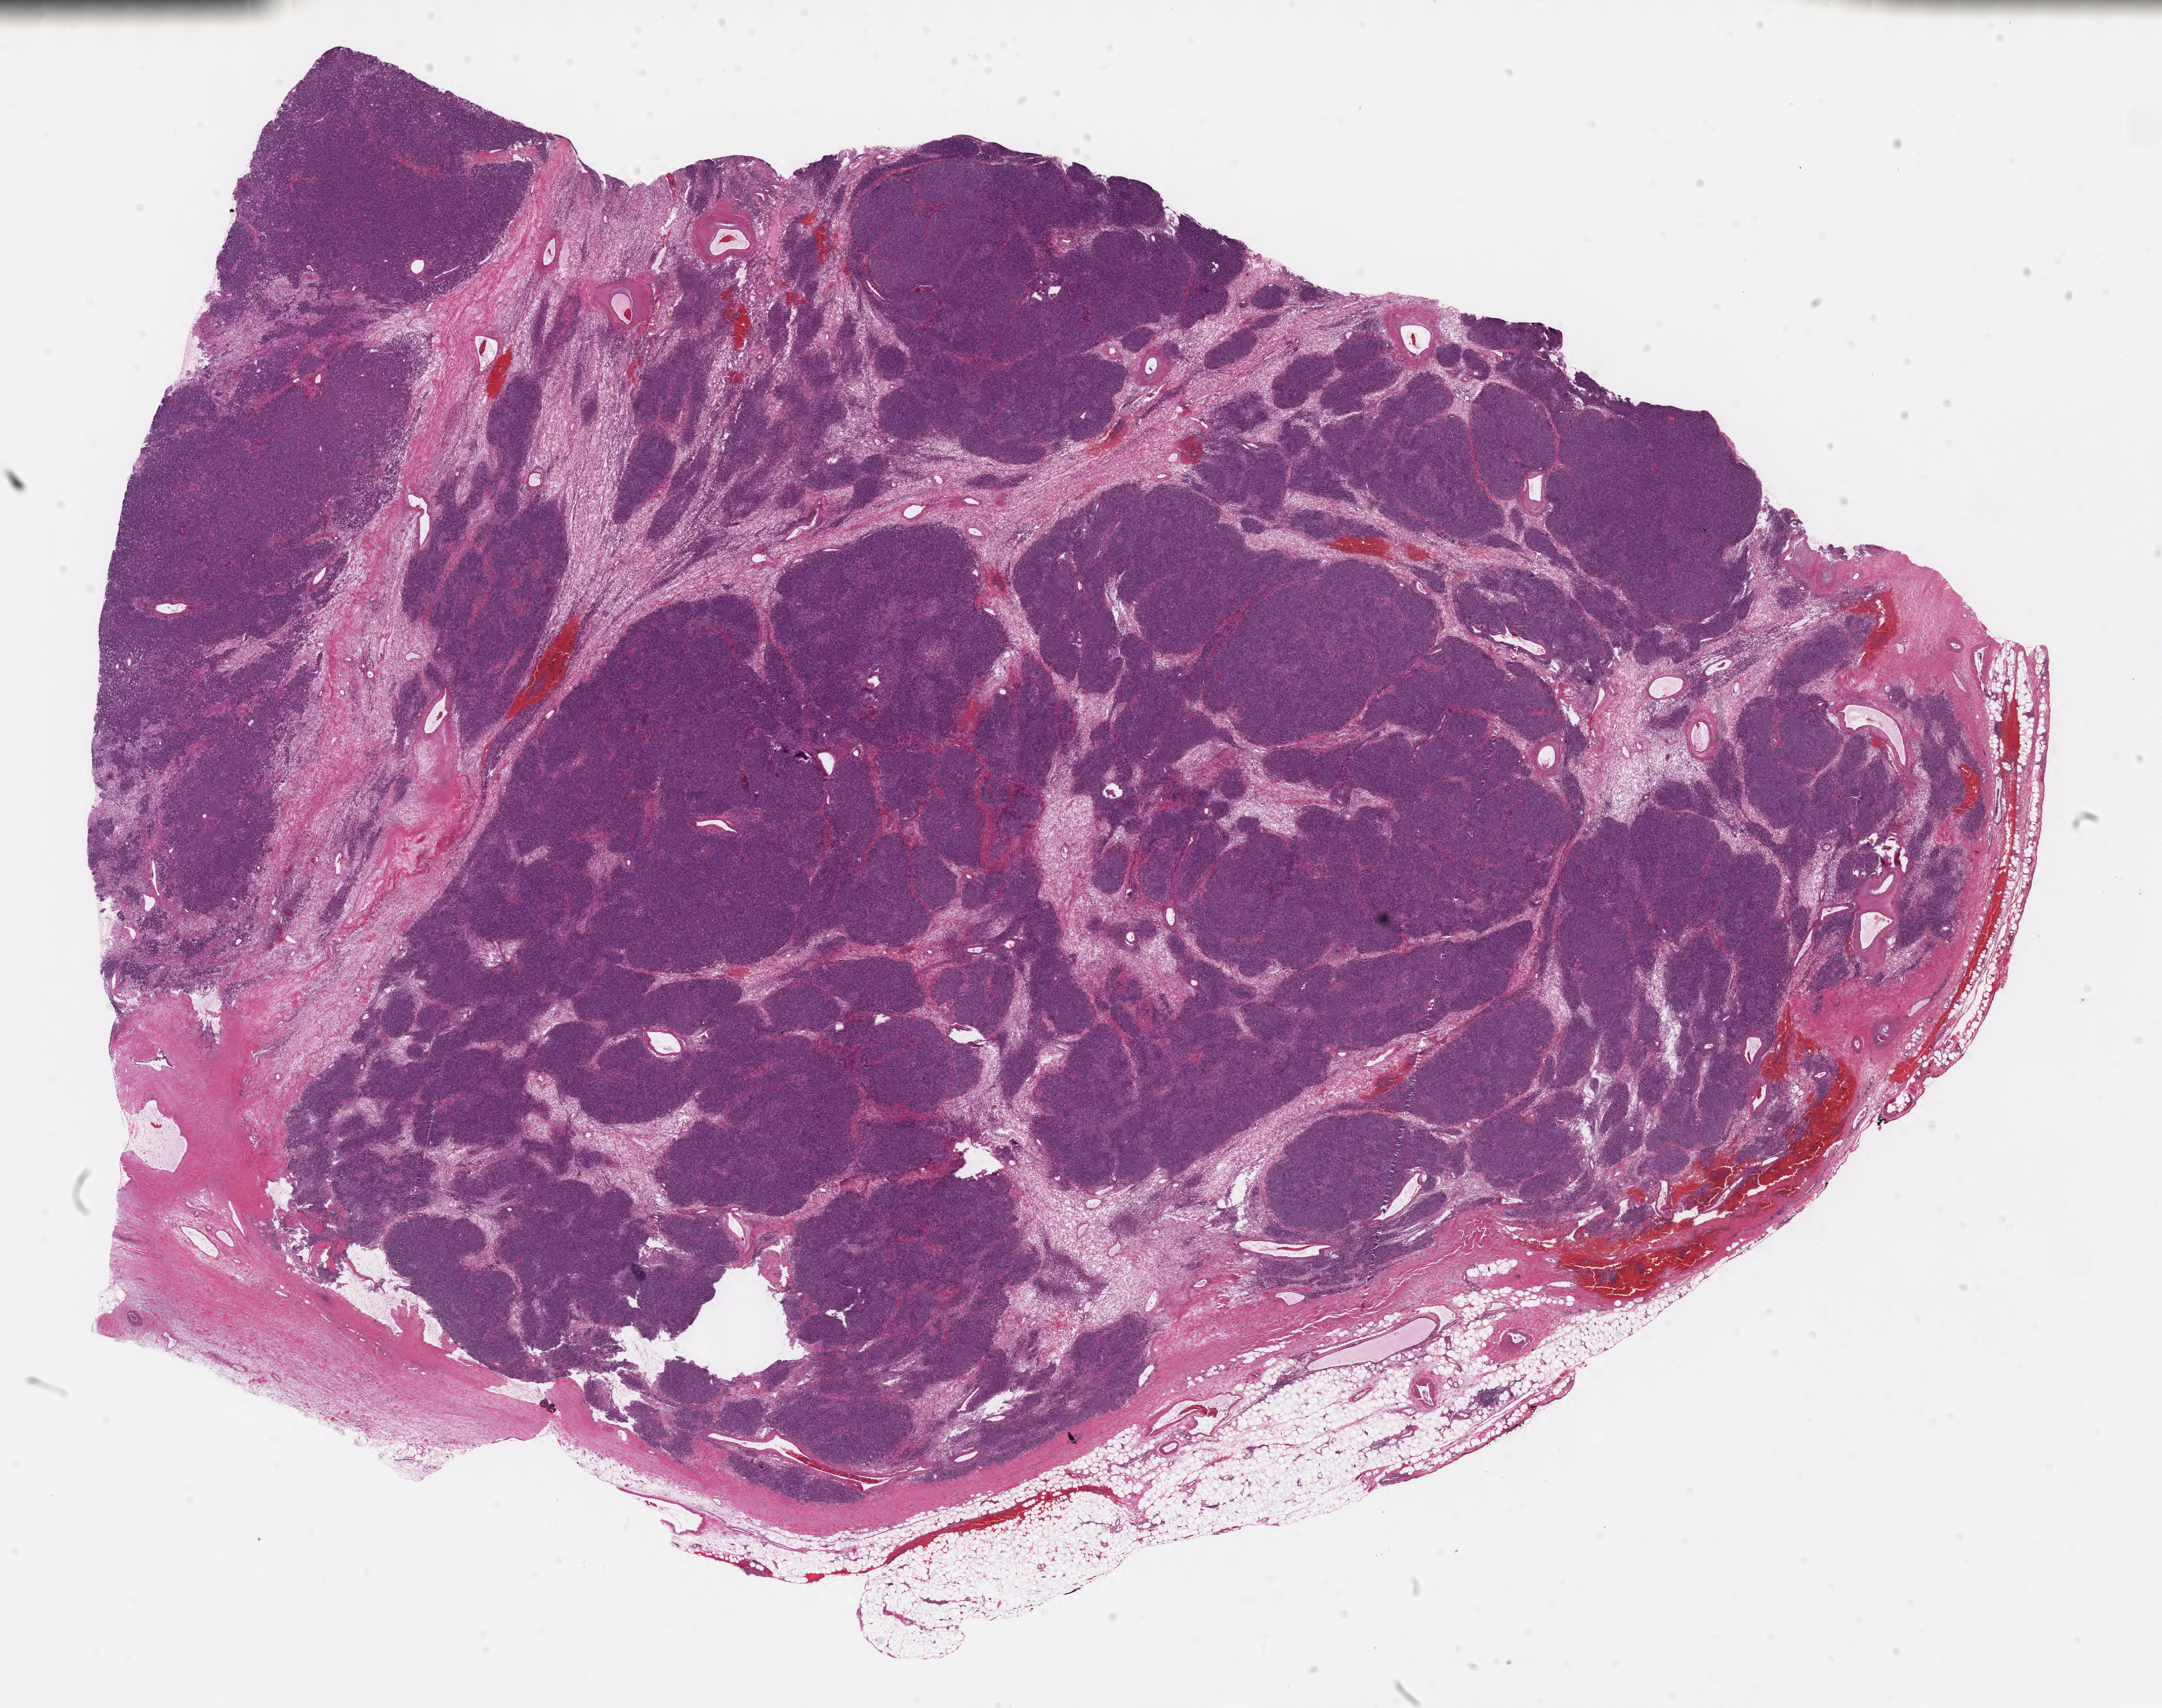
Hematoxylin and eosin (H&E) stained whole-slide image — a low-resolution overview of the entire scanned area, about 26.2 x 20.7 mm; FFPE section; thymus, primary tumour sample. Male, age 66 years at initial diagnosis.
* histologic diagnosis: Thymoma, type A, malignant